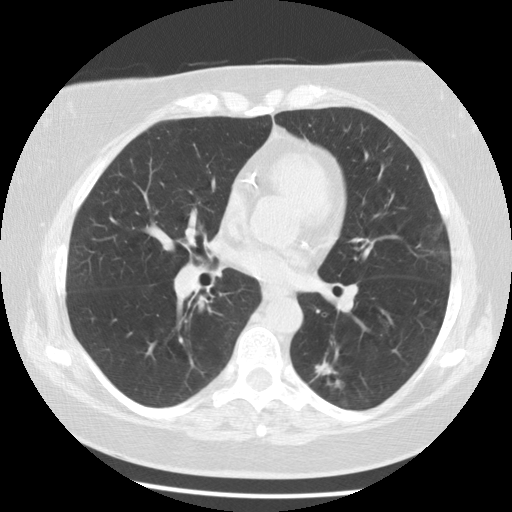
Axial slice from a low-dose chest CT screening exam. Third screening round (two years after baseline). Lung window (W 1500 / L -600 HU). 2.5 mm slice thickness. Standard (soft-tissue) reconstruction kernel (STANDARD). 120 kVp. Slice 59 of 116 in the series. 512 × 512 image matrix. Female, age 59 years at enrolment.
• Expert-annotated lung lesion, box from (x=293, y=348) to (x=358, y=406) px.
• The screening reader recorded 6 non-calcified nodules or masses ≥4 mm on this exam (right lower lobe, right upper lobe, right lower lobe, right lower lobe, left lower lobe, left lower lobe); which of them this box marks is not recorded.
• Official screen result: positive, other.
• Lung cancer was diagnosed 56 days after this screen: adenocarcinoma, NOS, left lower lobe, poorly differentiated (G3), stage IA (AJCC 6th edition), 15 mm at pathology.